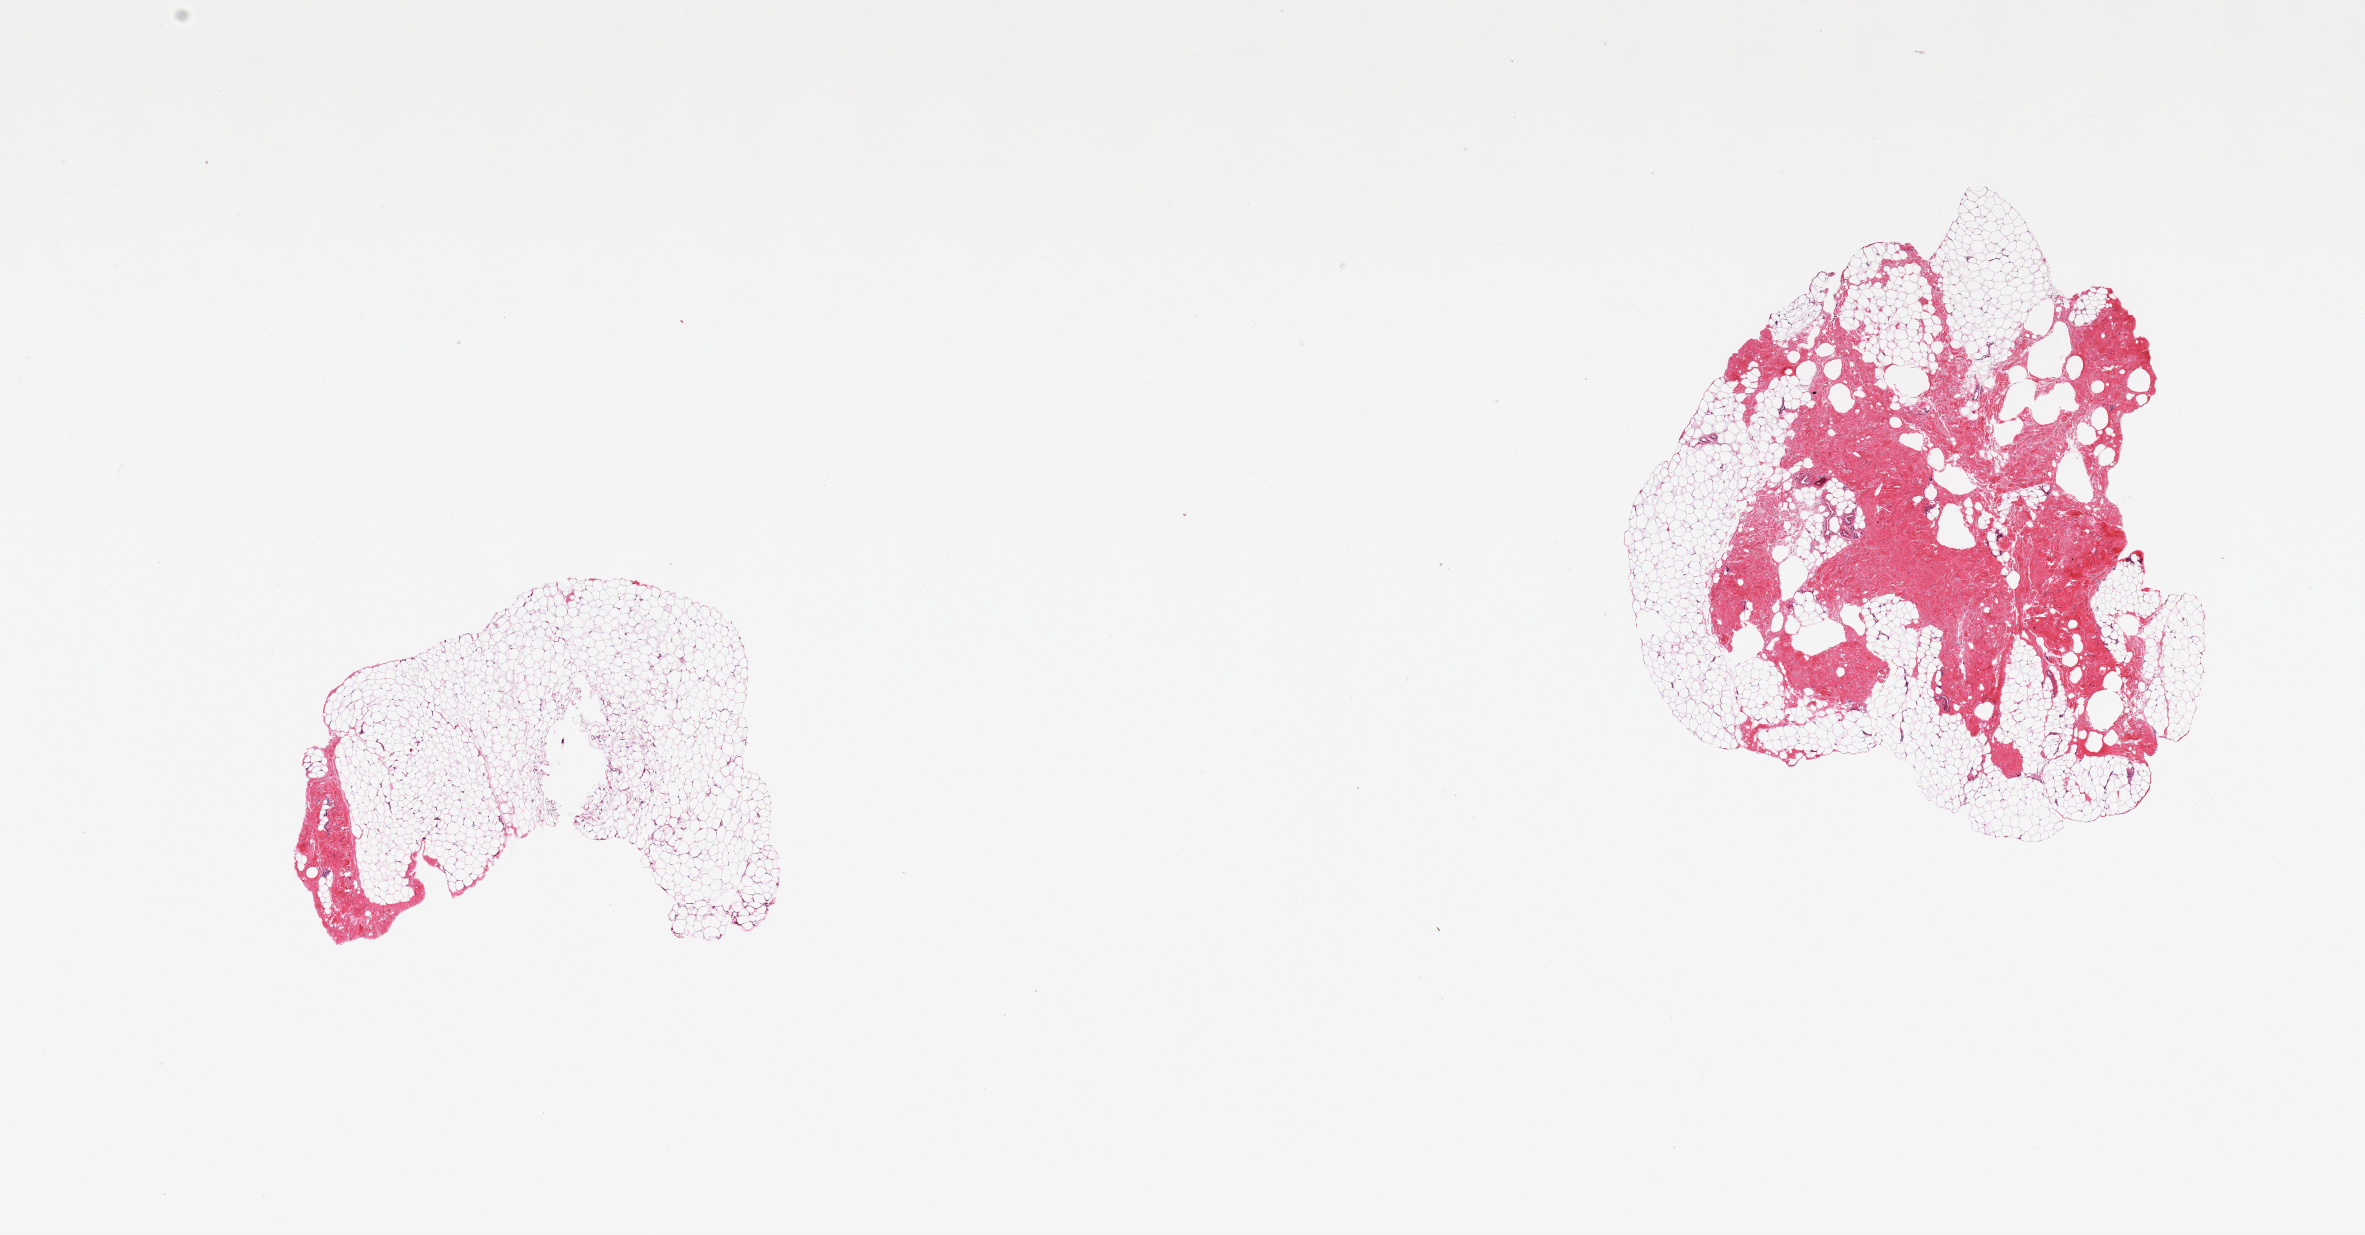
Digitized H&E-stained section — a low-resolution overview of the entire scanned area, about 18.7 x 9.8 mm; PAXgene-fixed, paraffin-embedded tissue; target tissue: breast; donor tissue sample. Donor sex: male.
Review note (as recorded): 2 pieces; fat and dense fibrous stroma, no ductal elements in this section.